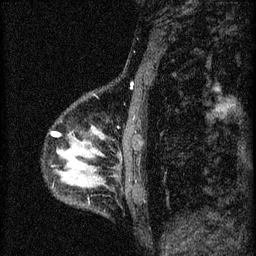
Breast MRI (dynamic contrast-enhanced), one sagittal slice; slice 10 of 60 in the series (ordered by position); 3 images stored at this slice position (order not interpretable as contrast timing); 1.5 T; TE 4.2 ms, TR 8.2 ms; 256 × 256 image matrix, field of view 180 × 180 mm. Patient: female, 37 years.
Outlined on this slice (semi-automatic segmentation, software-assisted and operator-edited):
- analysis volume of interest (the breast-tissue region the enhancement analysis was run in; not a lesion): bounding box <53,126,109,189> (left, top, right, bottom; pixels)
- tumour enhancement mask (voxels above the 70 % enhancement threshold inside the analysis volume of interest): <53,132,59,137>